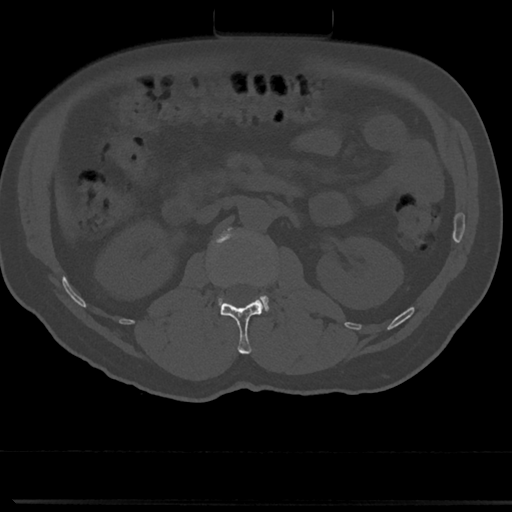
CT including the spine, one axial slice; slice 53 of 817 in the series (ordered by position); bone window (W 1800 / L 400 HU); 0.5 mm slice thickness; 512 × 512 image matrix, field of view 355 × 355 mm. Male patient, age 61 years. From the clinical record (not read from this slice): primary cancer: prostate.
Outlined on this slice (semi-automatically segmented with operator editing):
- L1 vertebra: bounding box [x1, y1, x2, y2] px = [220, 299, 264, 354]
- L2 vertebra: [212, 228, 269, 313]